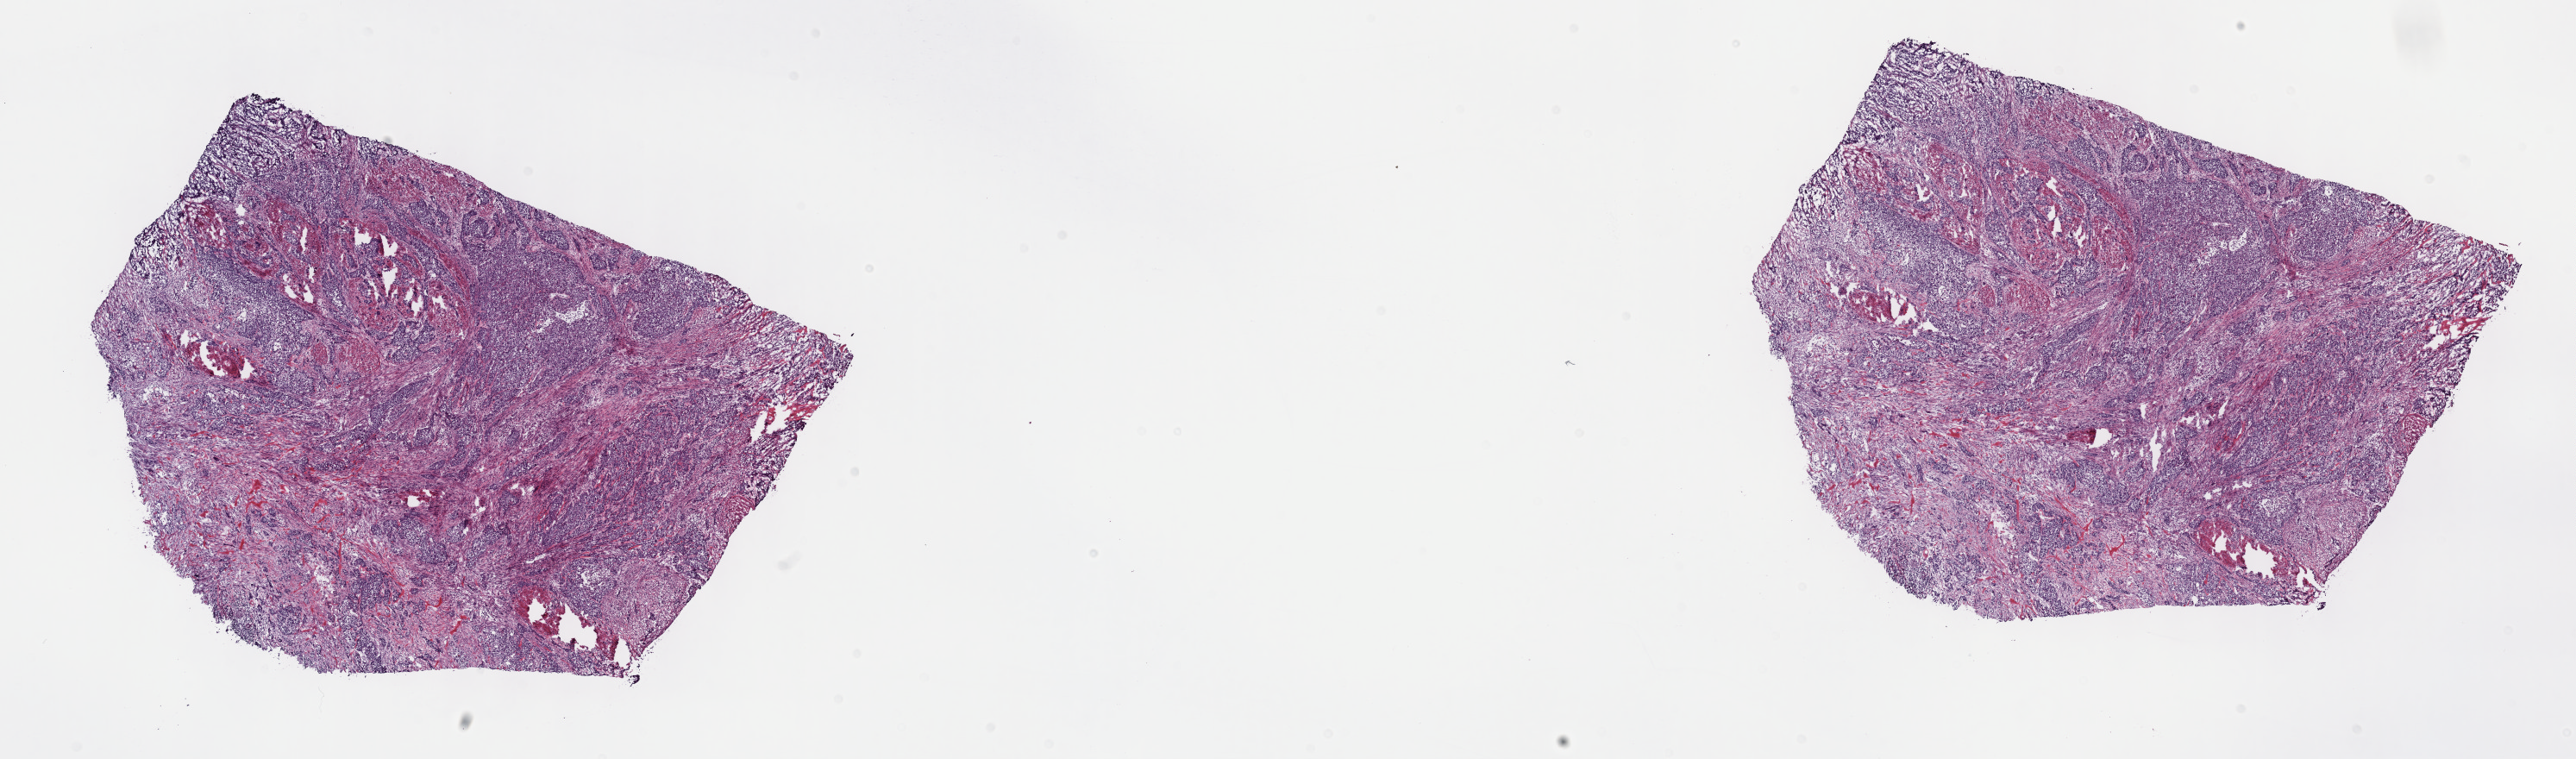
Whole-slide histology image, H&E, a low-resolution overview of the entire scanned area, about 24.2 x 7.1 mm (acquisition: 40x scan). Frozen section from the top of the tissue portion. Primary tumour sample from the bladder. Male, age 65 years at initial diagnosis. Histologic grade: high grade. Pathologist review of this section (percent, as recorded): tumour cells 70%, tumour nuclei 70%, normal cells 0%, stromal cells 30%, necrosis 0%. Infiltration values recorded for this section: lymphocyte infiltration 4%, monocyte infiltration 1%, neutrophil infiltration 5%.
Pathologic diagnosis: Transitional cell carcinoma. Lymph nodes positive (case pathology): 3 of 108 examined. AJCC pathologic stage: IV (6th edition).